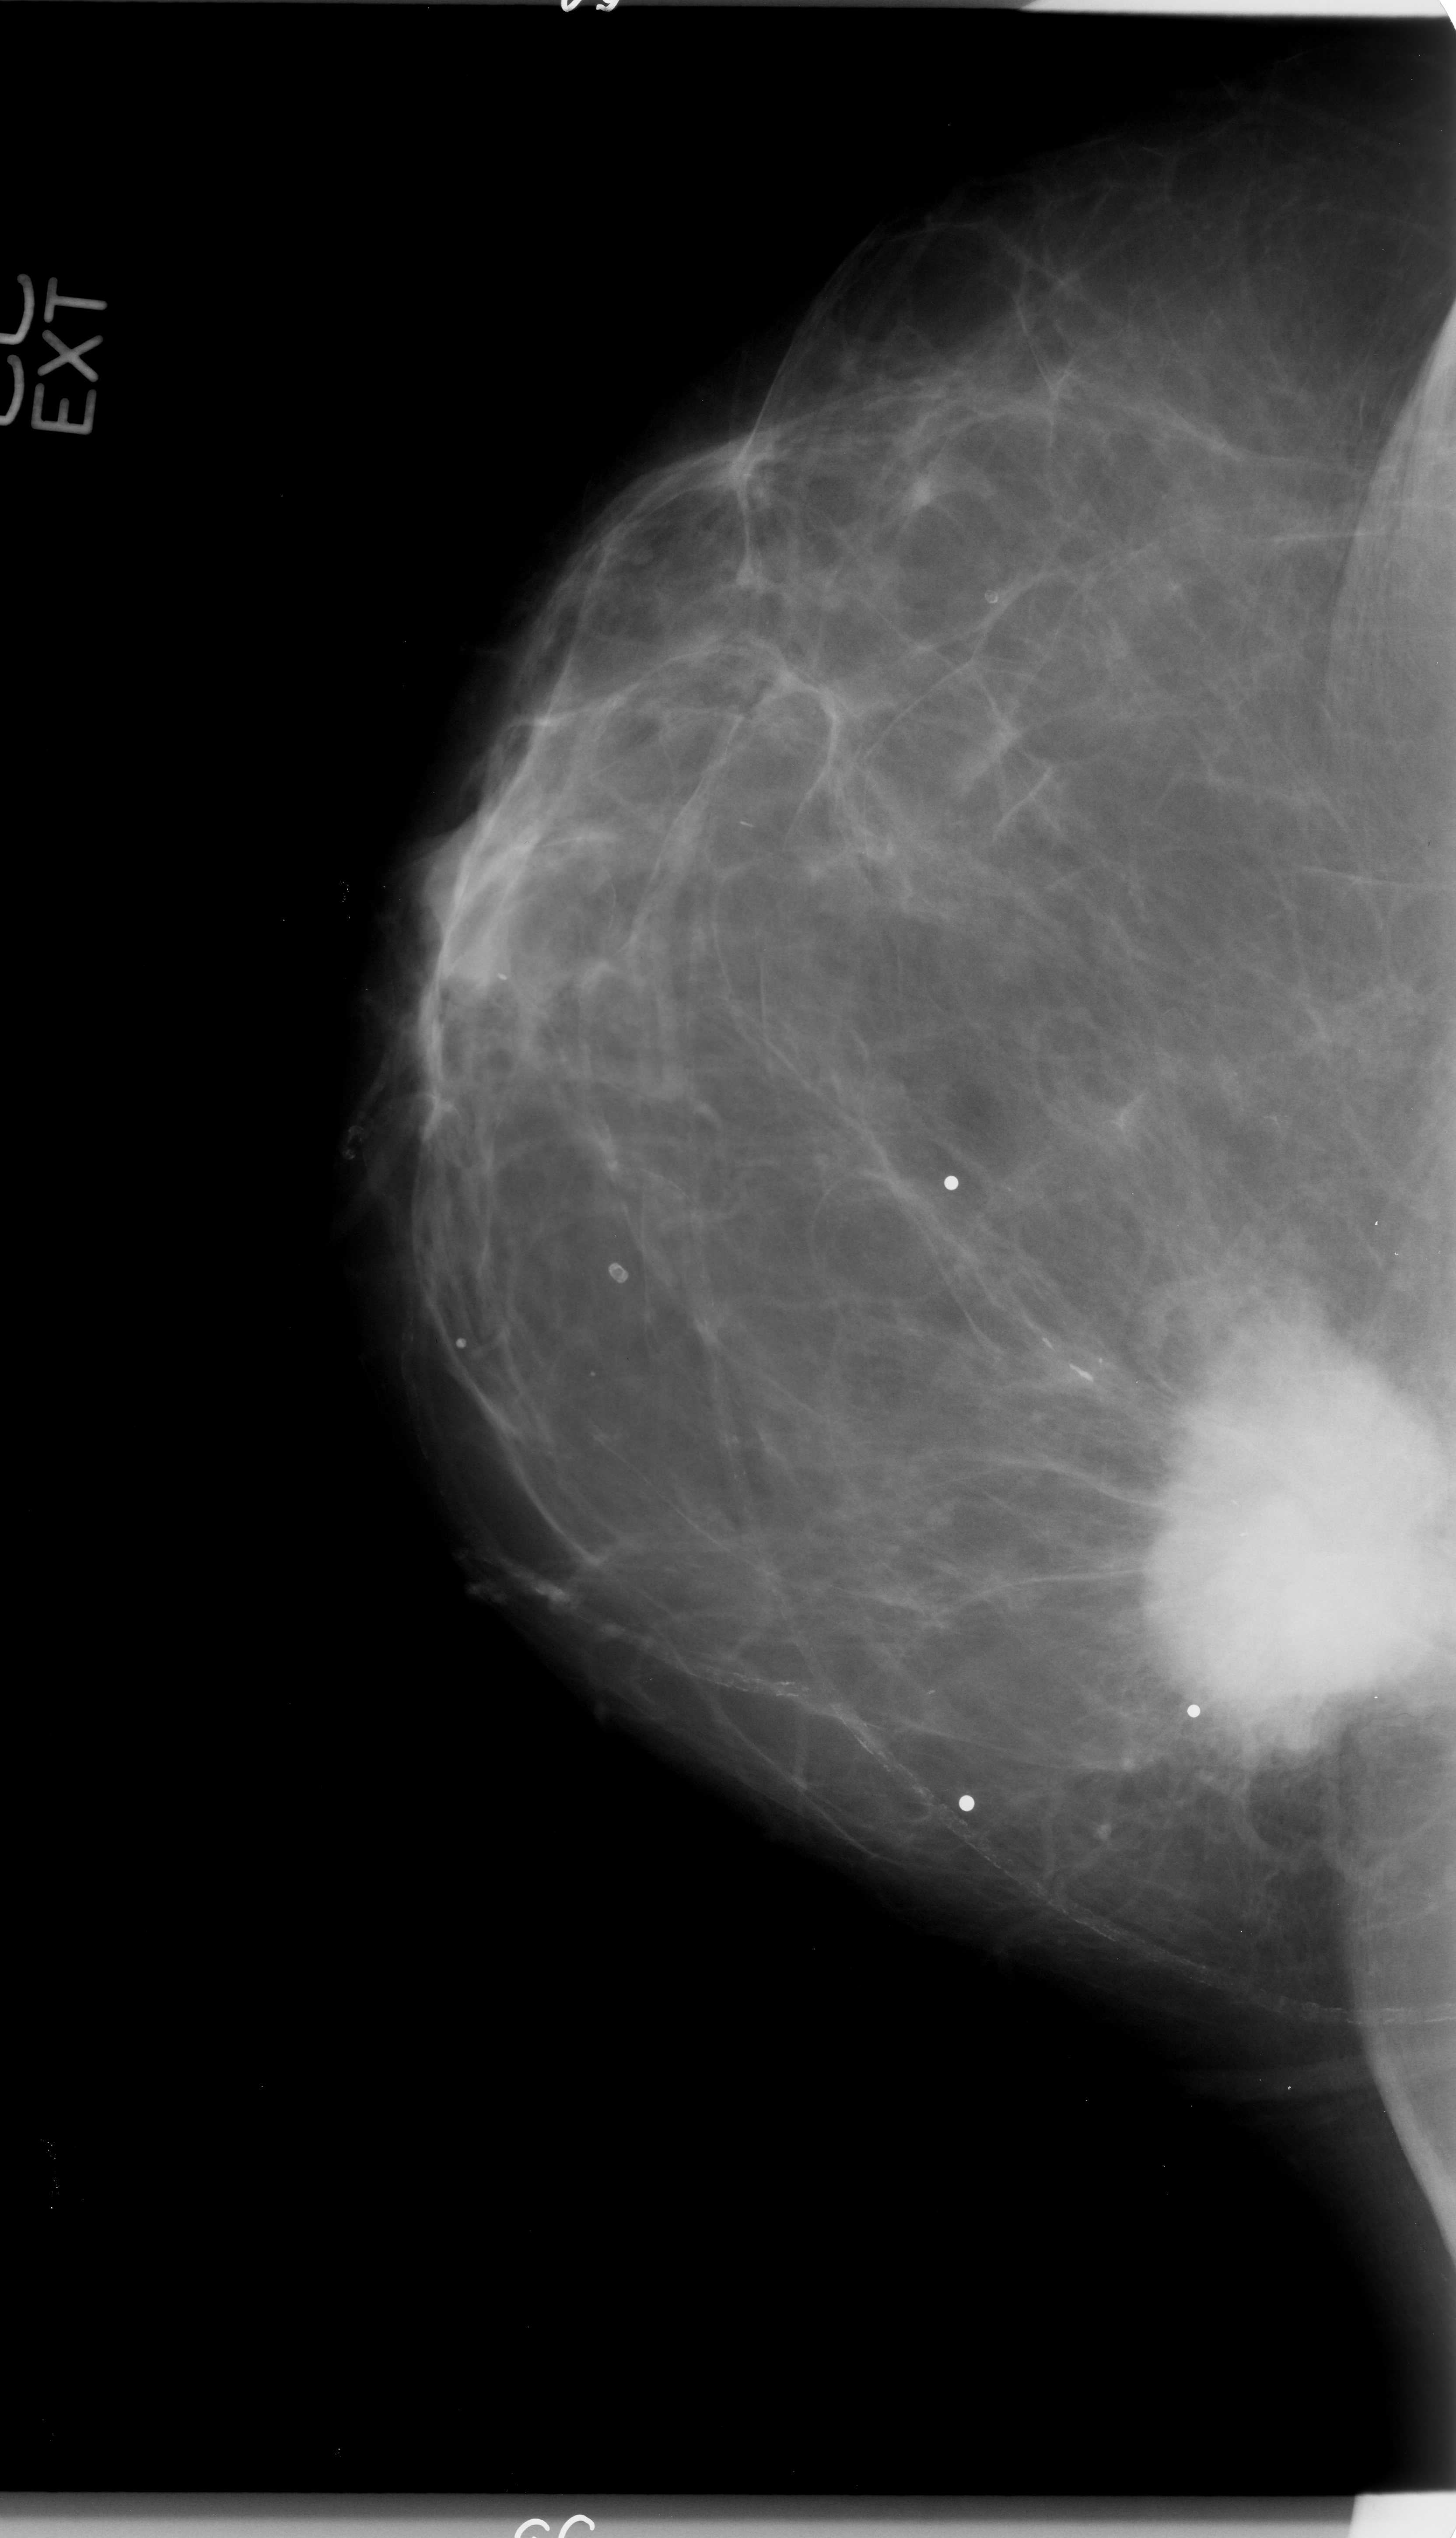
Scanned film-screen mammogram; right breast; CC view; BI-RADS breast density category 1 (scale 1–4); 1456 × 2538 image matrix.
Expert-marked regions of interest on this image (one box per marked abnormality):
- mass, shape irregular / architectural distortion, margins spiculated; BI-RADS assessment category 4; pathology (as recorded): malignant: box from (x=1160, y=1367) to (x=1436, y=1729) px